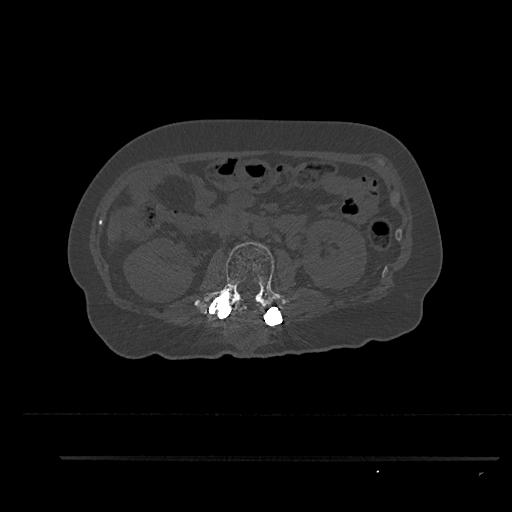
CT including the spine, one axial slice; slice 160 of 797 in the series (ordered by position); reconstruction kernel Br40s/3; 120 kVp; bone window (W 1800 / L 400 HU); 0.5 mm slice thickness; 512 × 512 image matrix, field of view 408 × 408 mm. Patient: female, 44 years. From the clinical record (not read from this slice): primary cancer: renal.
Structures marked on this image (semi-automatic segmentation, software-assisted and operator-edited):
- L2 vertebra: bounding box <194,242,284,319> (left, top, right, bottom; pixels)